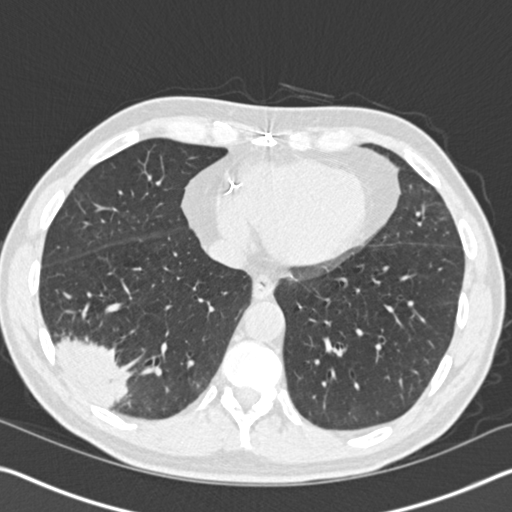
Low-dose screening chest CT, axial slice; baseline annual screen; lung window (W 1500 / L -600 HU); 2 mm slice thickness; standard (soft-tissue) reconstruction kernel (B30f). Male participant, aged 61 years at enrolment.
- Expert-annotated lung lesion, bounding box (x1, y1, x2, y2) in pixels: (28, 300, 147, 419).
- The exam's reader record, not a measurement of the box and not confirmed to be the same lesion: non-calcified nodule or mass ≥4 mm, right lower lobe, 52 × 36 mm, spiculated (stellate) margins, soft tissue attenuation.
- Official screen result: positive, change unspecified: nodule(s) >= 4 mm or enlarging nodule(s), mass(es), or other non-specific abnormalities suspicious for lung cancer.
- Later outcome: lung cancer diagnosed 392 days after this screen (after the second annual screen) — bronchiolo-alveolar adenocarcinoma, NOS, right lower lobe, moderately differentiated (G2), stage IIIB (AJCC 6th edition), 90 mm at pathology.